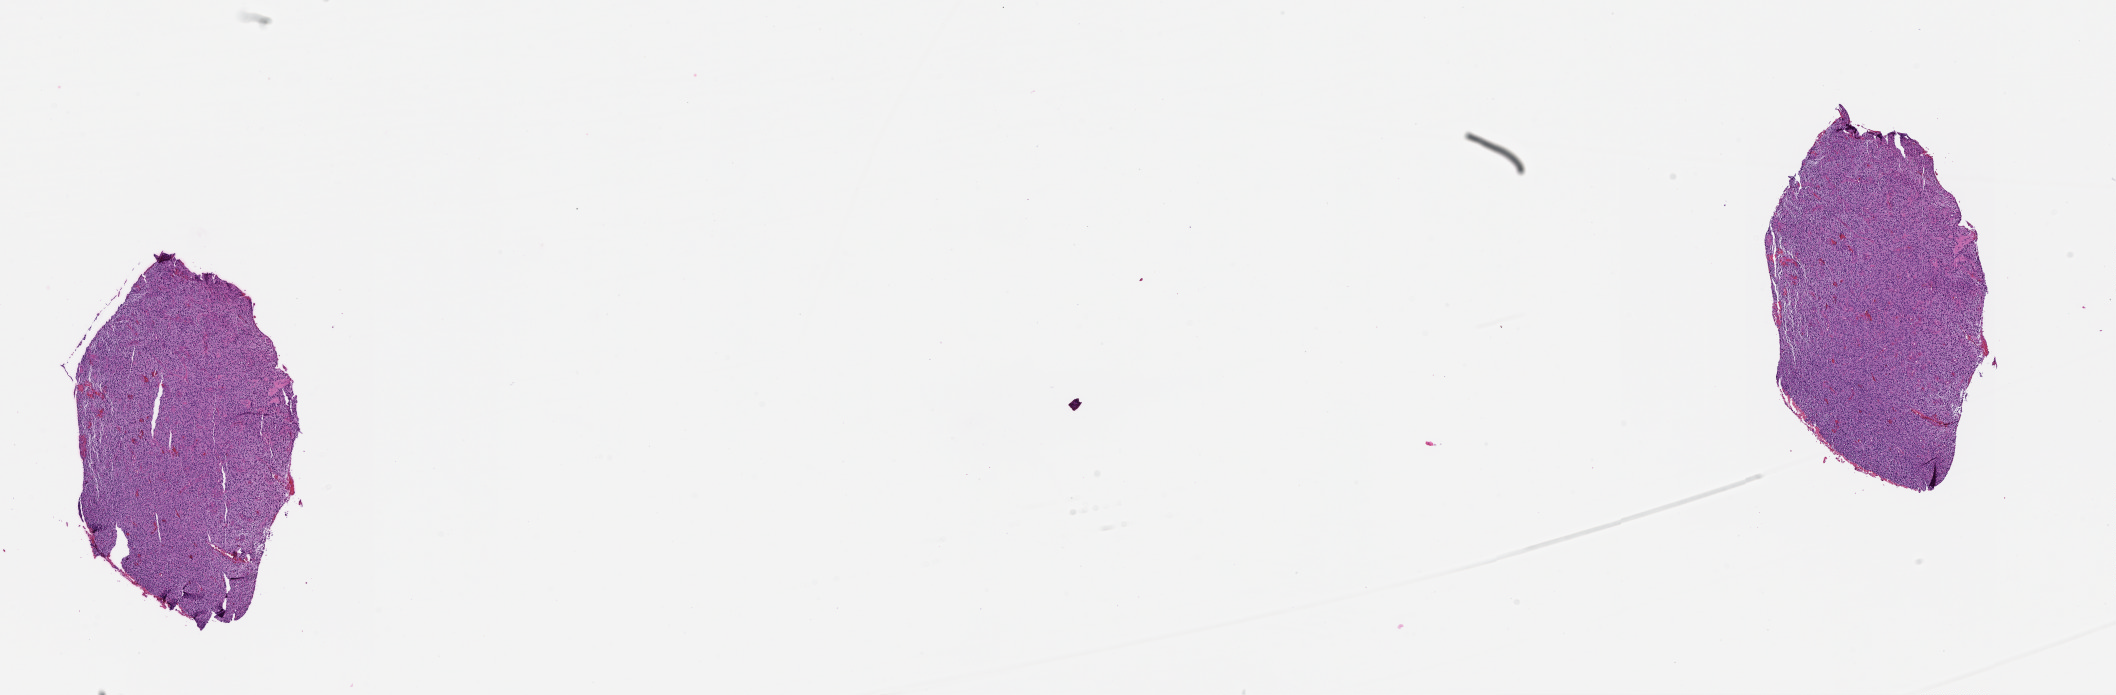
Digitized Hematoxylin and eosin (H&E) stained tissue section (whole slide), a low-resolution overview of the entire scanned area, about 17.0 x 5.6 mm (from a 20x scan). Tumour tissue sample, sampled site: brain. Female, 71 y/o. Pathologist review of this section (percent, as recorded): tumour nuclei 85%, necrosis 5%.
Primary tumour site (as recorded): frontal lobe. Histologic diagnosis: Glioblastoma.